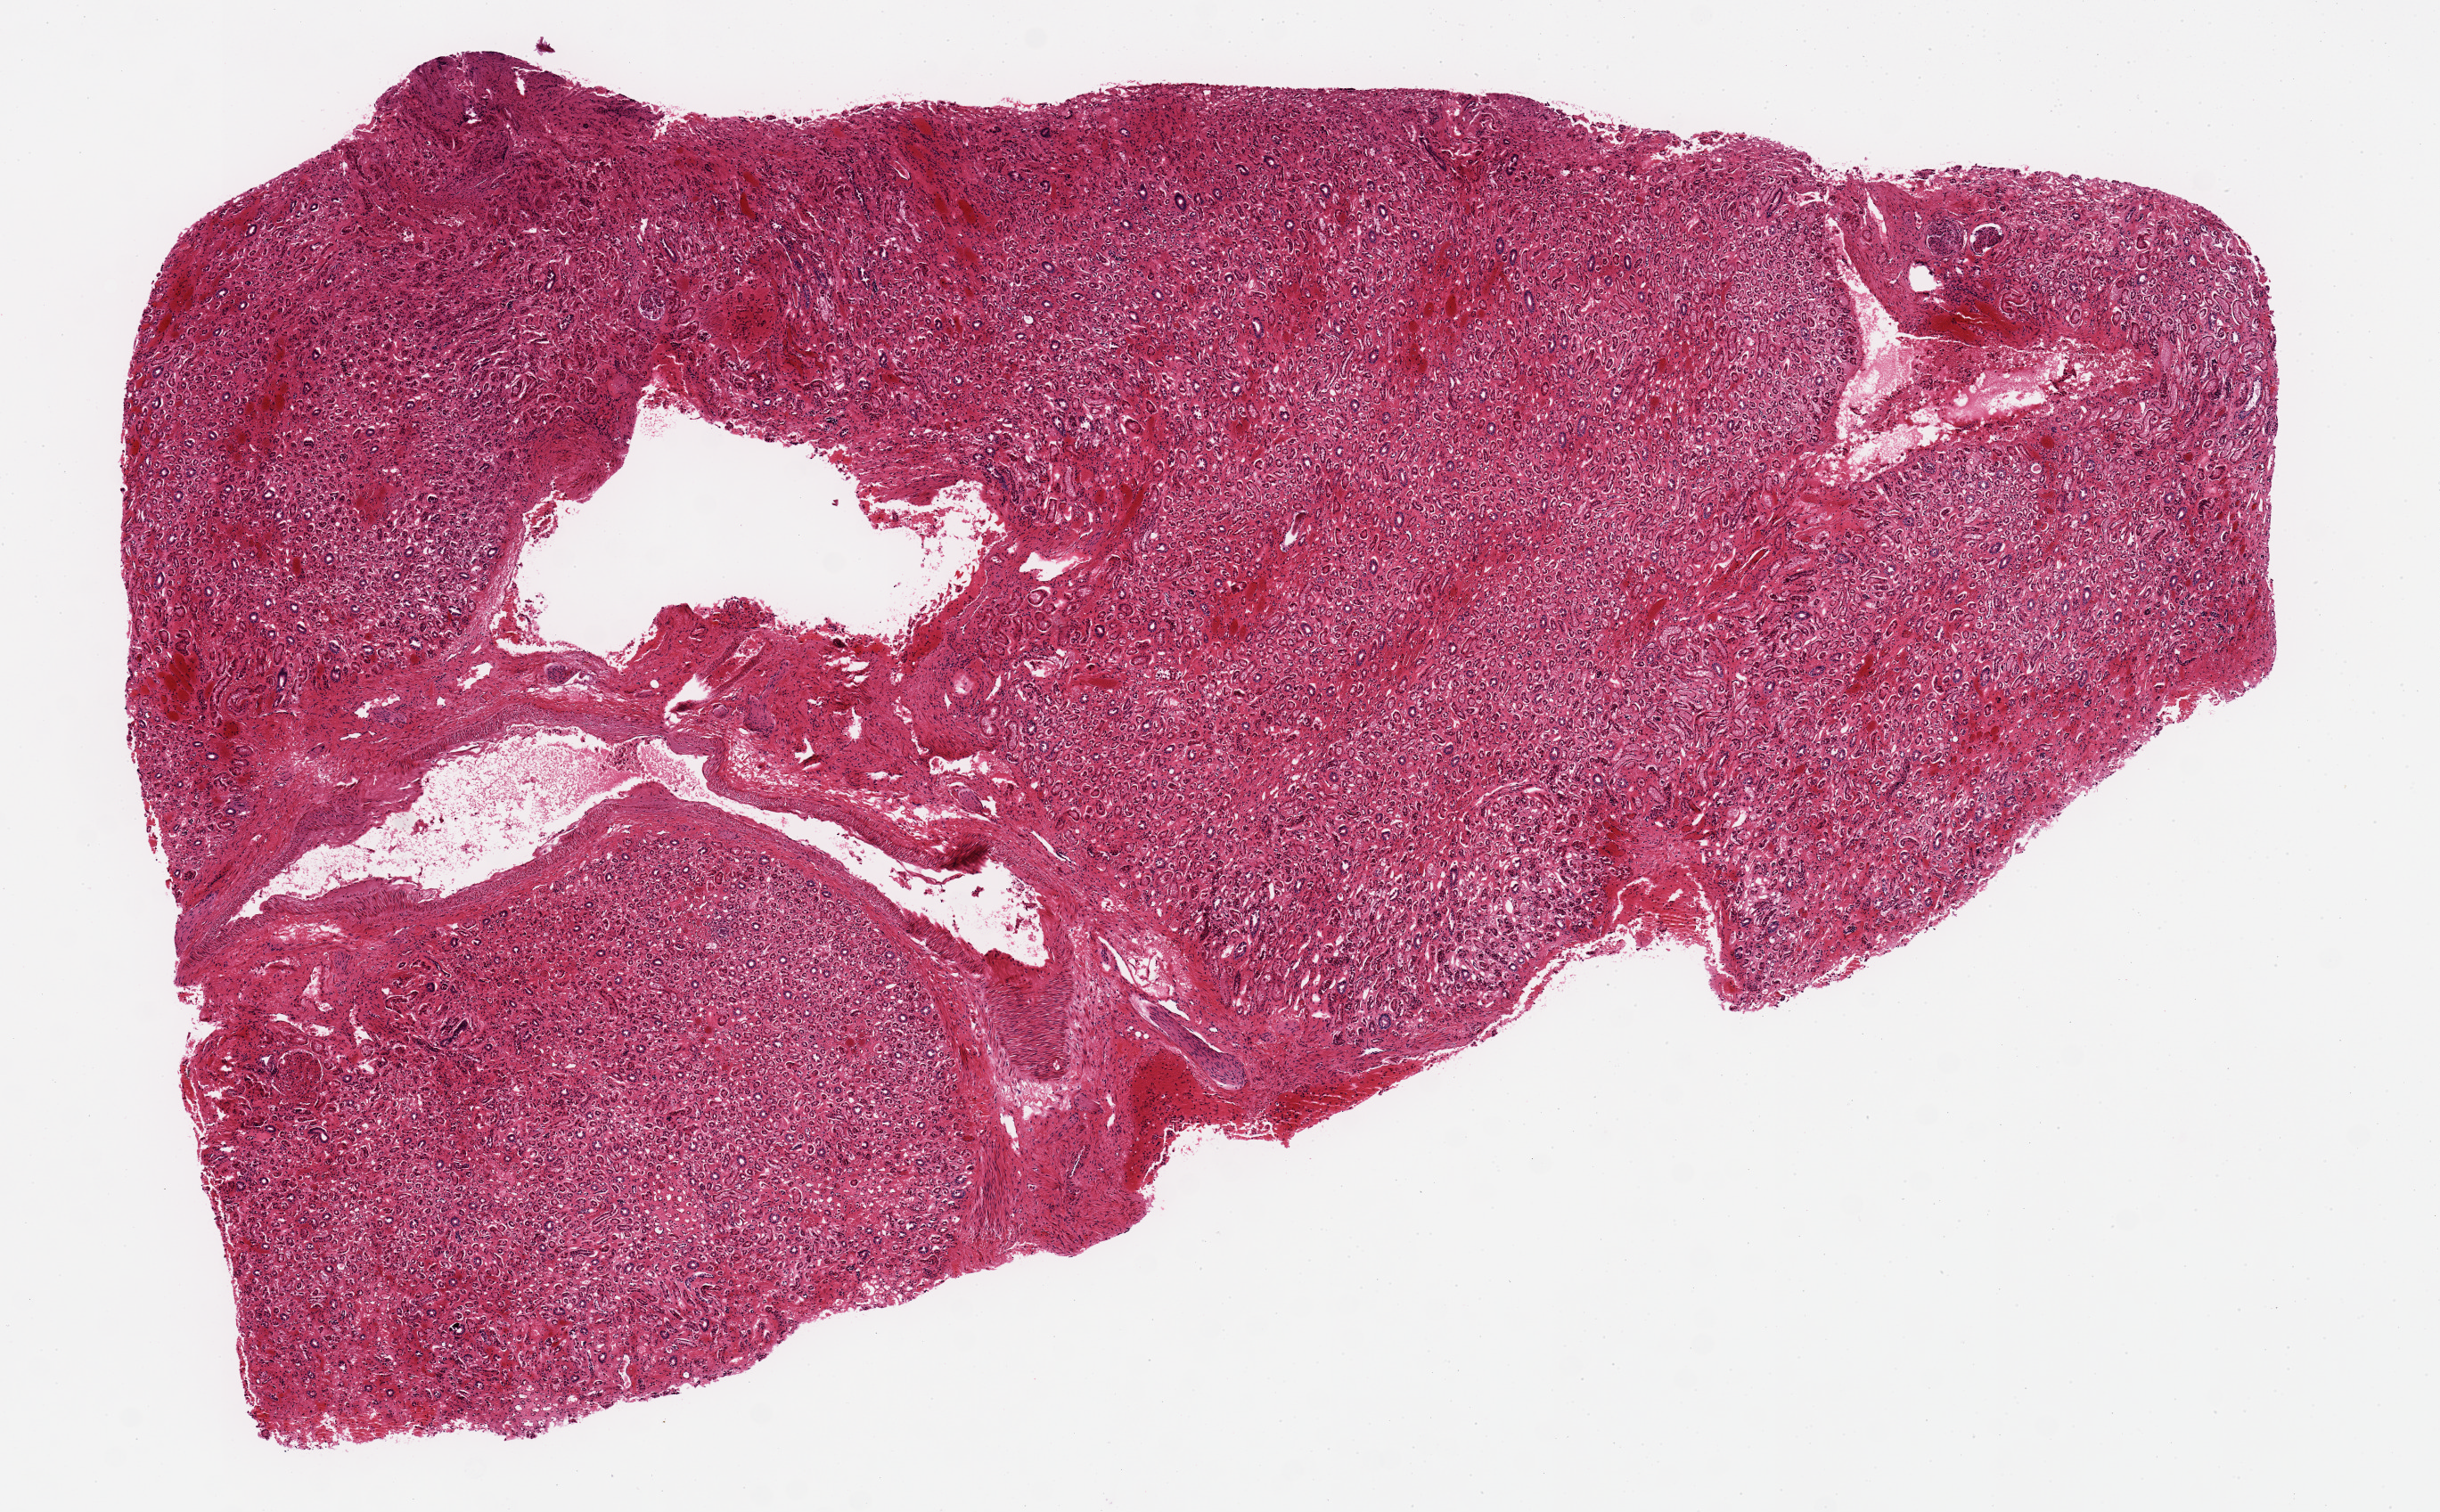
Hematoxylin and eosin (H&E) whole-slide image, brightfield — low-resolution overview of the scanned area, about 10.8 x 6.7 mm (acquisition: 20x scan), PAXgene-fixed, paraffin-embedded tissue, target tissue: renal medulla, tissue donor sample. Donor: male.
- pathologist's review note for this sample: 9.5x4.5mm. All tubules, no glomeruli